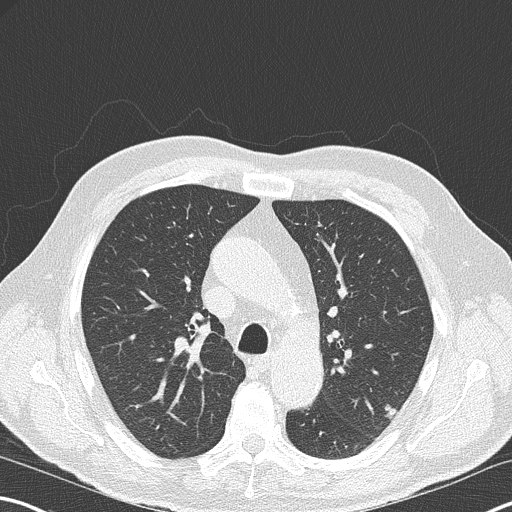
Low-dose screening chest CT, axial slice. Second annual screen. Lung window (W 1500 / L -600 HU). Lung (sharp) reconstruction kernel (B50f). Slice 72 of 178 in the series. 512 × 512 image matrix, field of view 344 × 344 mm. Male, age 67 years at enrolment. Former smoker at enrolment.
Expert reader's lesion annotation, bounding box <369,396,410,428> (left, top, right, bottom; pixels). The exam's reader record, not a measurement of the box and not confirmed to be the same lesion: non-calcified nodule or mass ≥4 mm, left upper lobe, 9 × 6 mm, poorly defined margins, soft tissue attenuation, pre-existing on the prior screen: no. Lung cancer was diagnosed 418 days after this screen: squamous cell carcinoma, large cell, nonkeratinizing, NOS, left upper lobe, moderately differentiated (G2), stage IA (AJCC 6th edition), 15 mm at pathology.